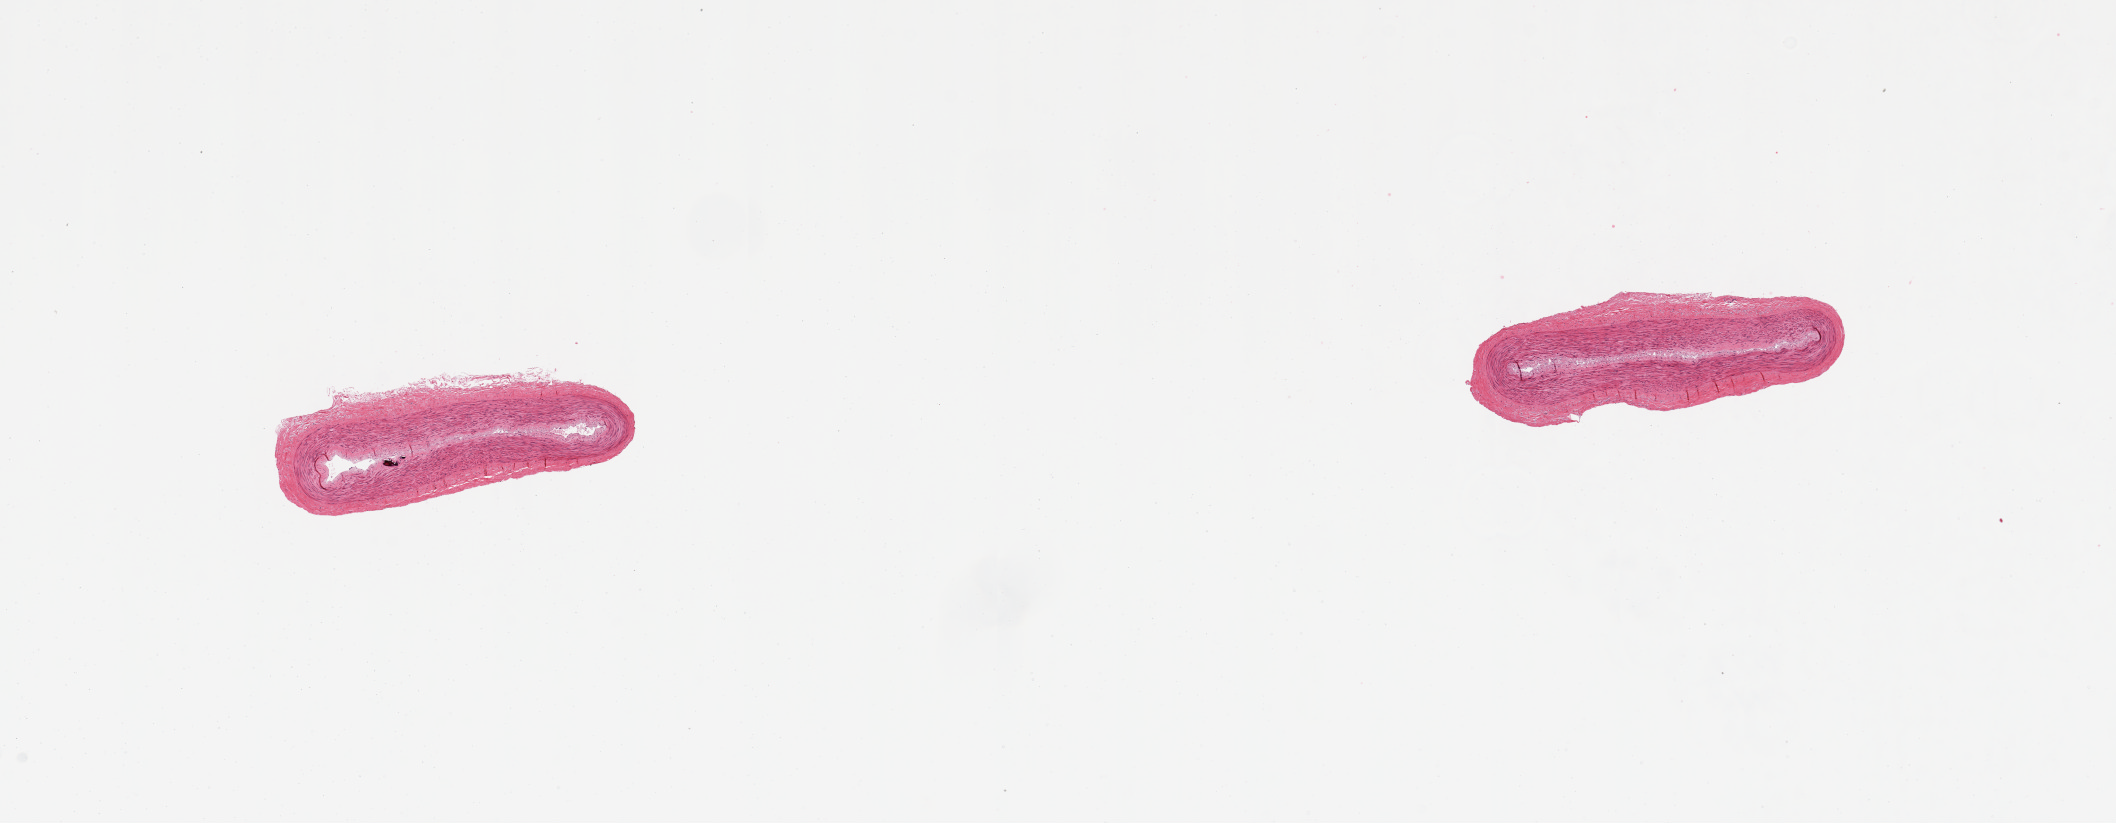
Digitized hematoxylin and eosin (H&E)-stained section, brightfield, whole scanned area (about 16.7 x 6.5 mm, from a 20x scan) shown as a low-resolution overview, PAXgene-fixed paraffin-embedded (PFPE) section, sampled site (target tissue): tibial artery, donor tissue sample. Male donor.
Pathologist's review note for this sample: 2 pieces; well dissected; small focus of calcium; no plaque.